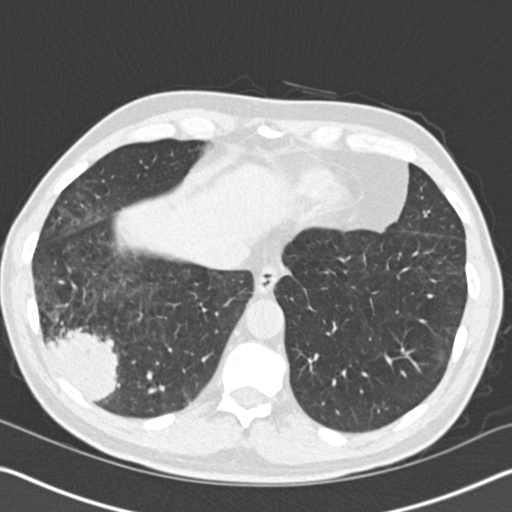
Axial slice from a low-dose chest CT screening exam; baseline annual screen; lung window (W 1500 / L -600 HU); 2 mm slice thickness; 120 kVp. Male, age 61 years at enrolment.
• Lesion marked by an expert reader, bounding box <17,284,141,416> (left, top, right, bottom; pixels).
• The exam's reader record, not a measurement of the box and not confirmed to be the same lesion: non-calcified nodule or mass ≥4 mm, right lower lobe, 52 × 36 mm, spiculated (stellate) margins, soft tissue attenuation.
• Participant outcome: lung cancer diagnosed 392 days after this screen (after the second annual screen) — bronchiolo-alveolar adenocarcinoma, NOS, right lower lobe, moderately differentiated (G2), stage IIIB (AJCC 6th edition), 90 mm at pathology.